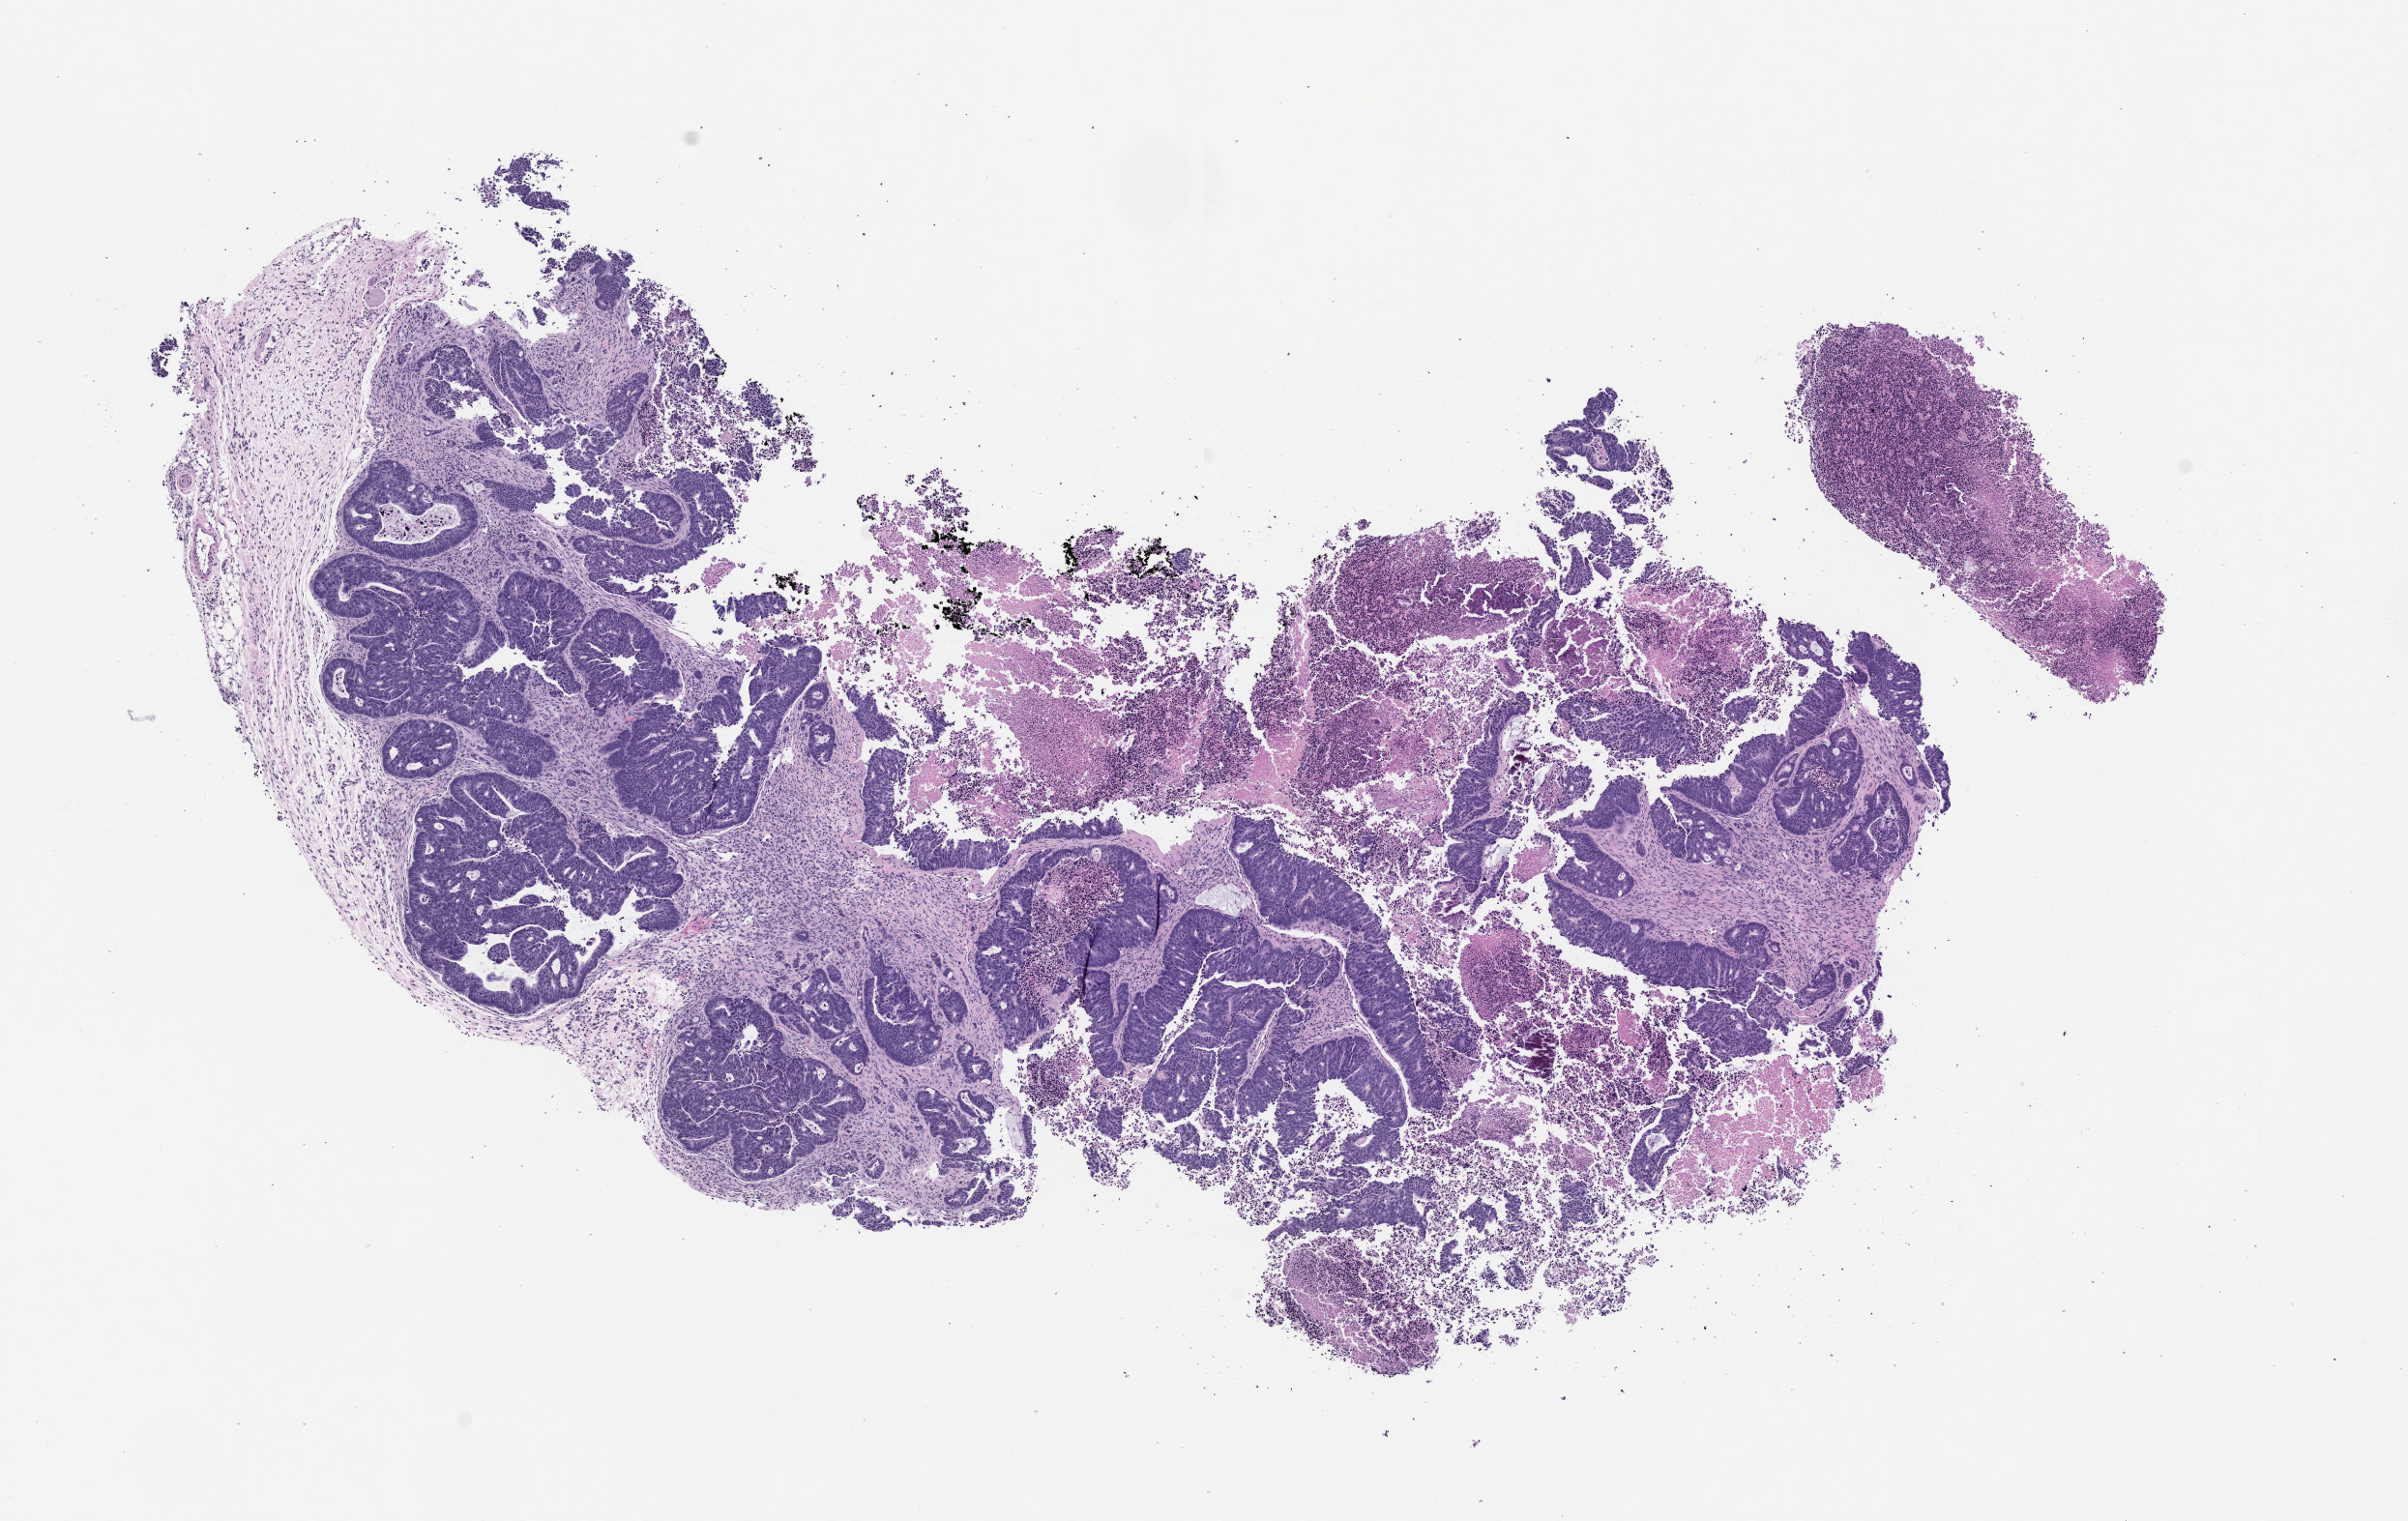
Whole-slide image, hematoxylin and eosin (H&E): patient-derived xenograft (human tumor grown in a mouse), passage 1 — a low-resolution overview of the entire scanned area, about 10.0 x 6.3 mm; formalin-fixed paraffin-embedded section; tumor site category: colon.
- originating patient diagnosis: Colon Adenocarcinoma